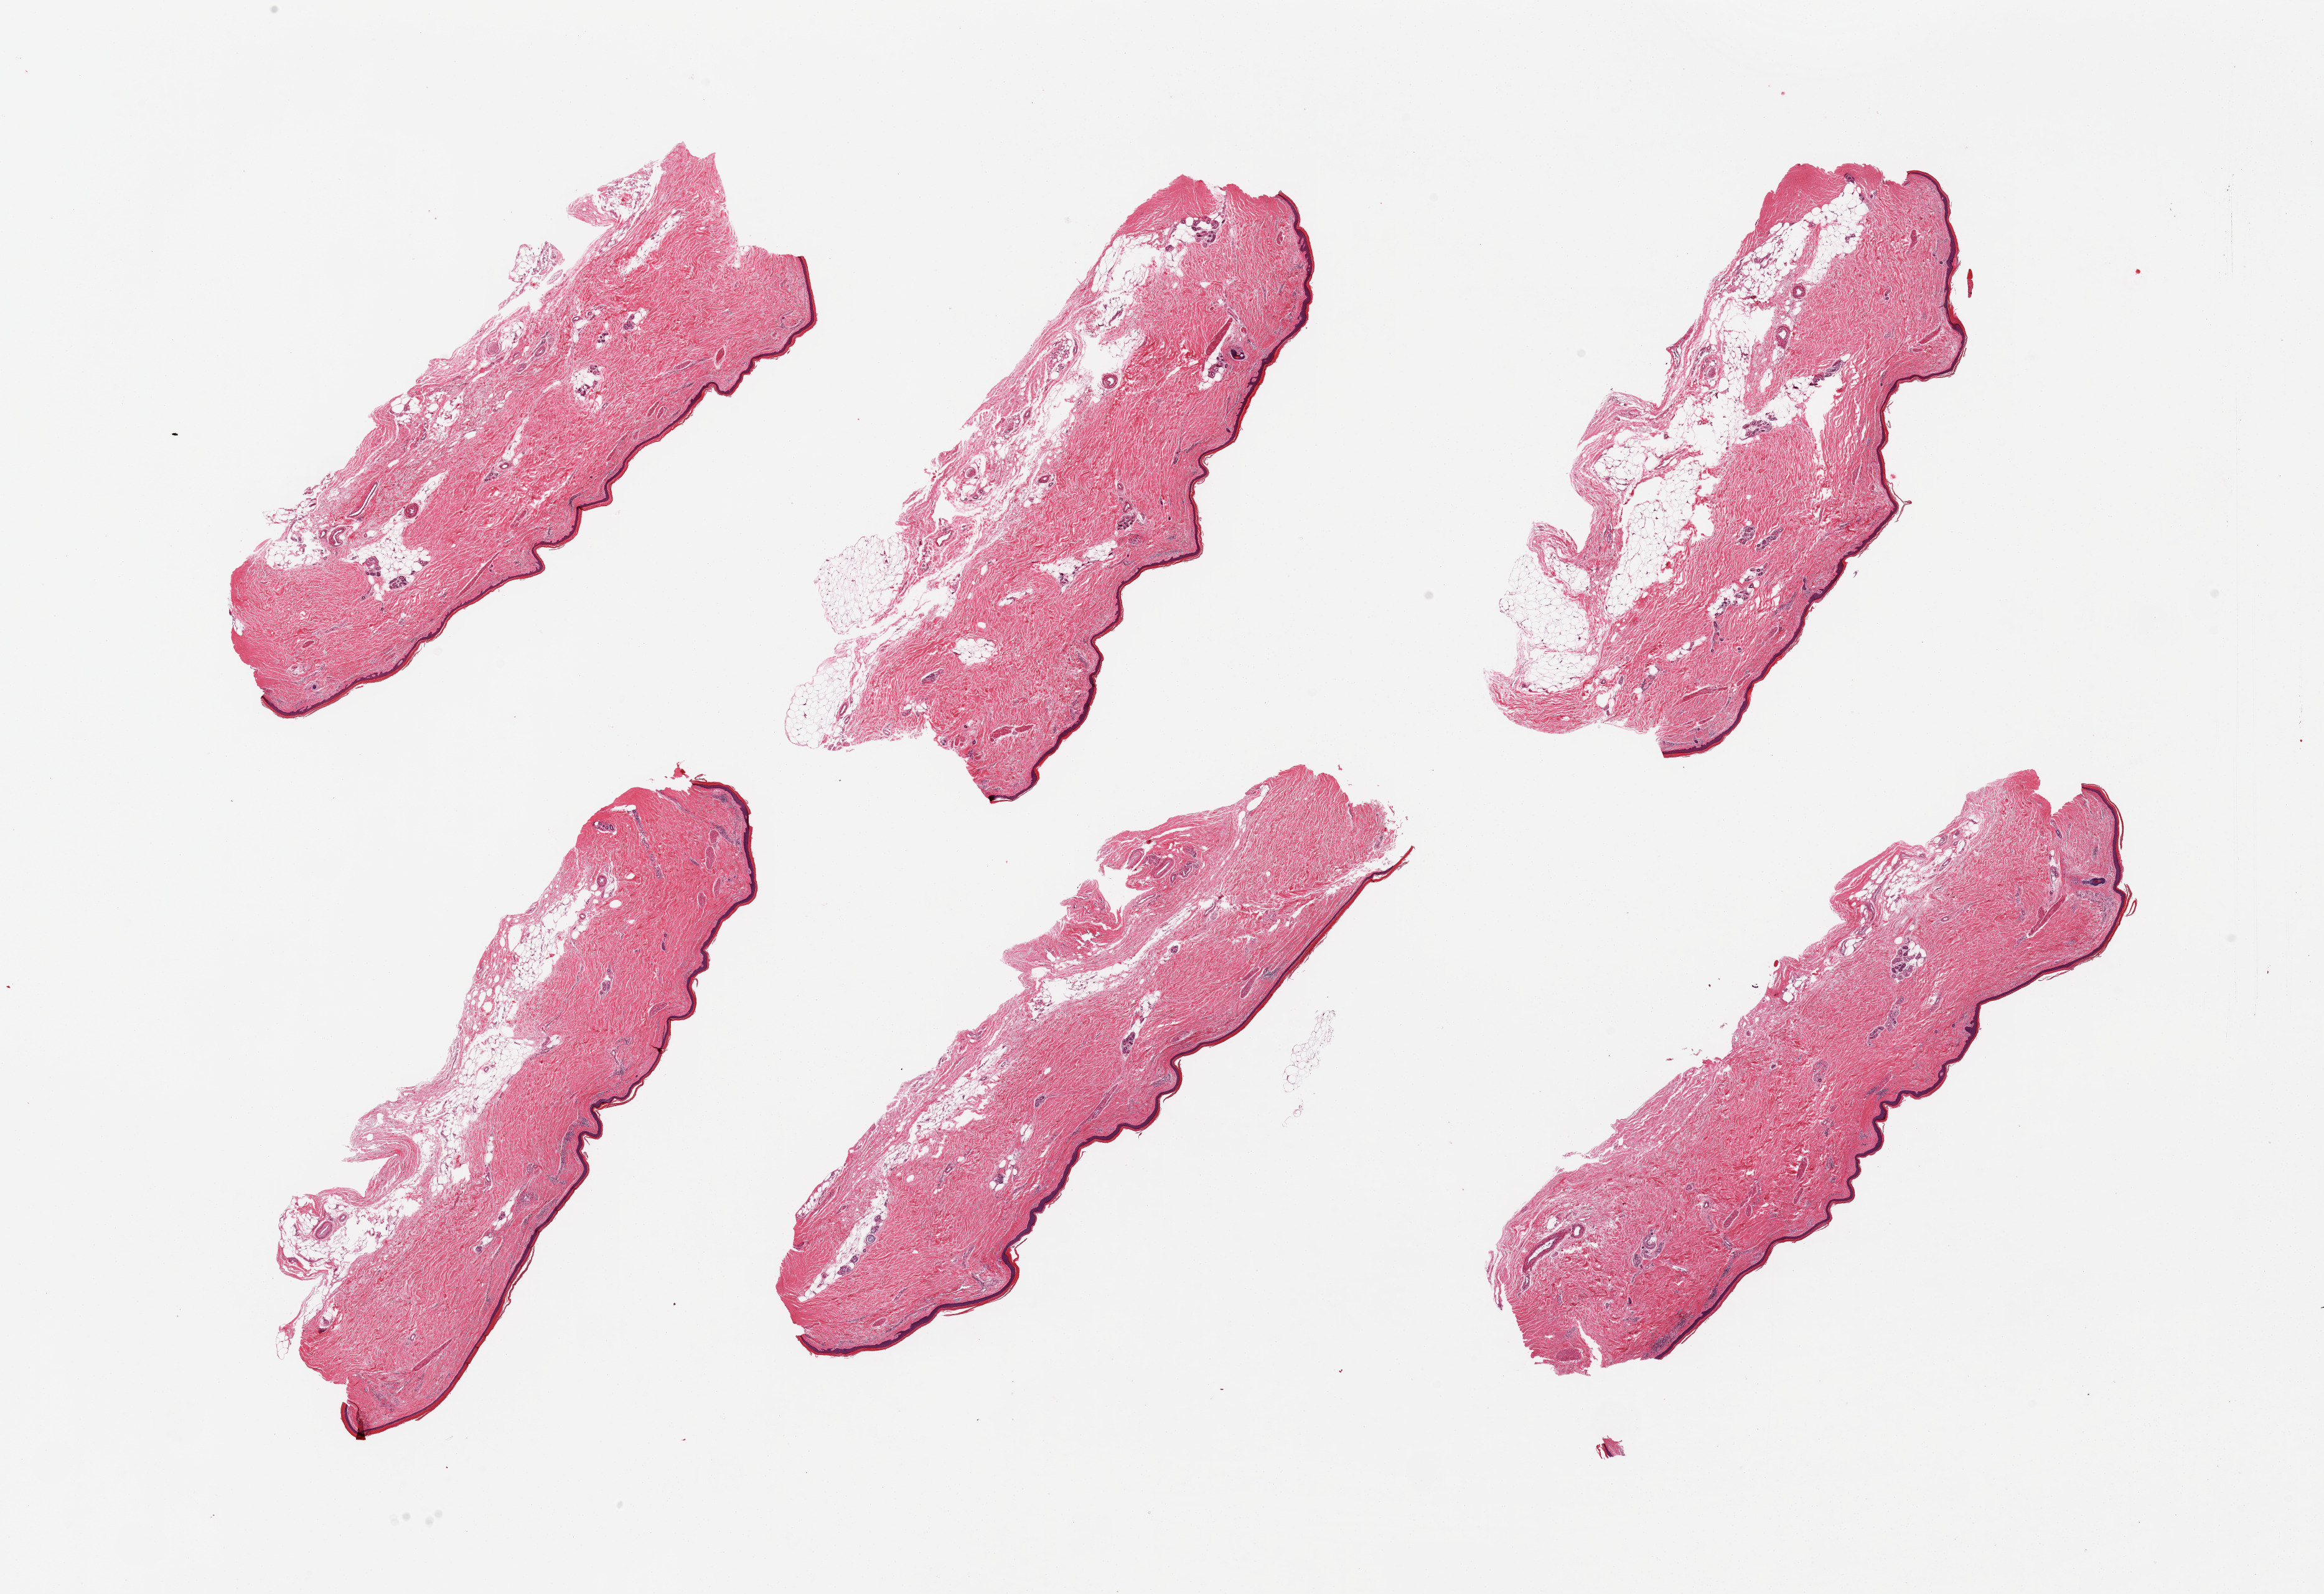
Whole-slide image, haematoxylin and eosin stain, low-resolution overview of the scanned area, about 29.5 x 20.3 mm (from a 20x scan), PAXgene-fixed, paraffin-embedded tissue, target tissue: skin of lower leg, donor tissue sample. Donor: male.
- reviewer comment on this tissue sample: 6 pieces; include variable amount of internal fat up to 30% (and minimal attached fat), epidermis measures 22-42 microns